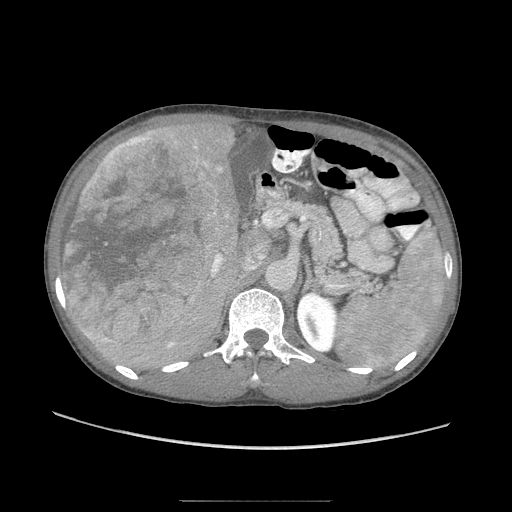
Contrast-enhanced abdominal CT (liver protocol), one axial slice. Slice 49 of 103 in the series (ordered by position). Reconstruction kernel STANDARD. 120 kVp. Soft-tissue window (W 400 / L 40 HU). 2.5 mm slice thickness. 512 × 512 image matrix, field of view 380 × 380 mm. From the clinical record (not read from this slice): diagnosis: hepatocellular carcinoma (patient treated with transarterial chemoembolisation; whether this scan precedes or follows treatment is not stated here); TNM stage (as recorded): Stage-IIIA; Child-Pugh class: A; tumour differentiation: moderately differentiated.
Annotated regions visible in this slice (semi-automatic segmentation, software-assisted and operator-edited):
- liver parenchyma outside the tumour (the mass and vessels are separate outlines, so this box may not span the whole liver): bounding box [x1, y1, x2, y2] px = [66, 114, 250, 378]
- mass: [62, 126, 220, 347]
- liver vessels: [208, 168, 220, 283]